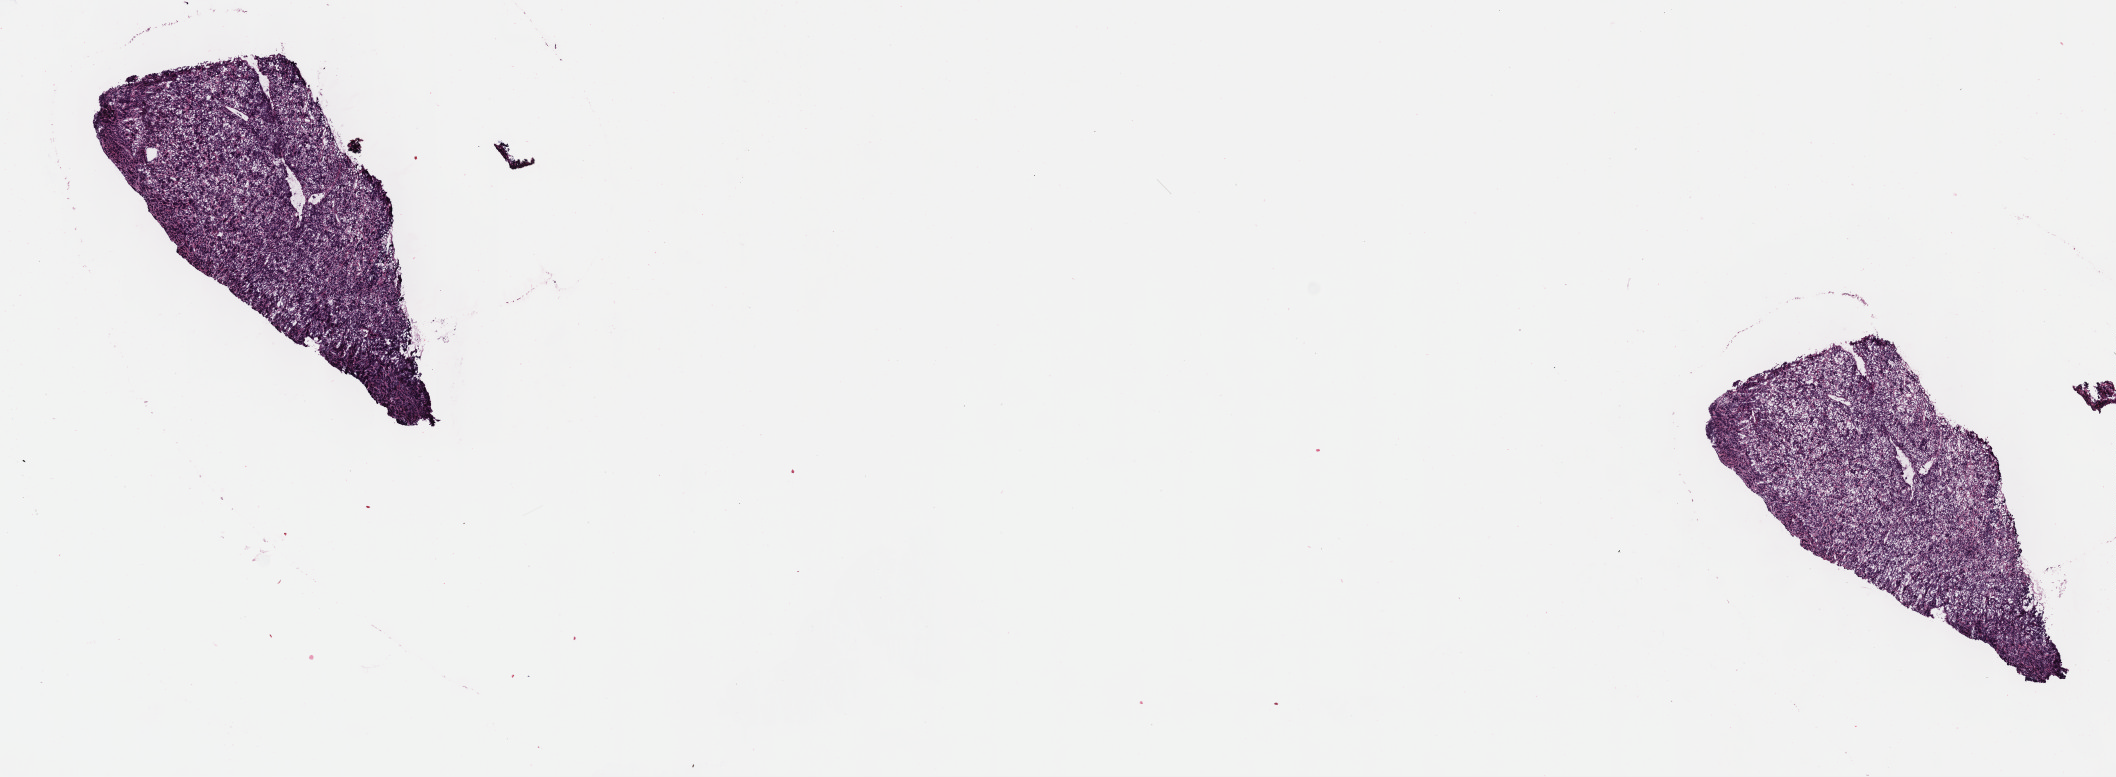
Whole-slide image, haematoxylin and eosin stain, low-resolution overview of the scanned area, about 17.1 x 6.3 mm. Frozen section. Primary tumor. Anatomic site: mouth. Female patient; age at initial diagnosis 7 years. Composition of this section per pathologist review: tumor cells 70%, tumor nuclei 80%, stromal cells 15%, necrosis 15%, normal cells 0%. Inflammatory infiltration, as recorded: lymphocyte infiltration 50%, monocyte infiltration 35%, neutrophil infiltration 0%.
Ann Arbor stage (patient): Stage III. Histologic diagnosis: Diffuse large B-cell lymphoma, NOS. Section: top of the tissue portion.